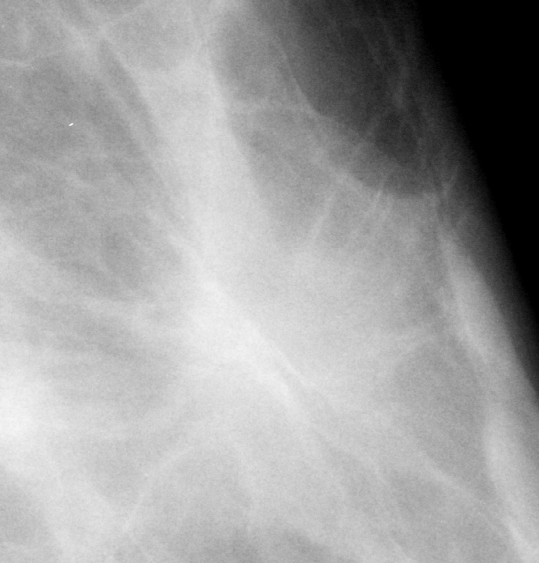
Crop from a digitized film mammogram around one marked abnormality, left breast, CC view.
Marked abnormality: mass, shape irregular / architectural distortion, margins obscured / ill defined / spiculated; BI-RADS assessment category 4; pathology result (as recorded, not read from the image): malignant.